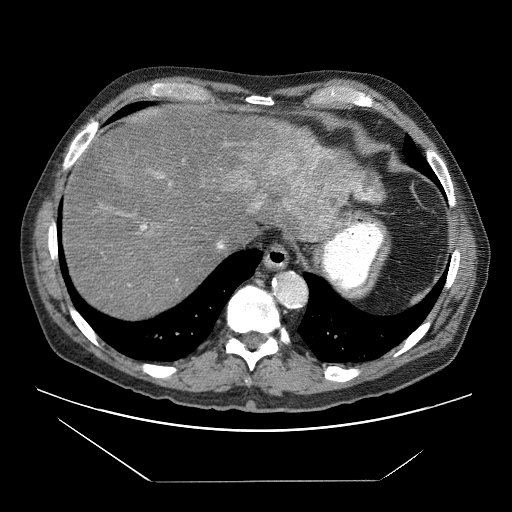
Contrast-enhanced abdominal CT (liver protocol), one axial slice; slice 60 of 83 in the series (ordered by position); soft-tissue window (W 400 / L 40 HU); 512 × 512 image matrix. From the clinical record (not read from this slice): diagnosis: hepatocellular carcinoma (patient treated with transarterial chemoembolisation; whether this scan precedes or follows treatment is not stated here); TNM stage (as recorded): Stage-IVB; Child-Pugh class: B; tumour differentiation: poorly differentiated.
Outlined on this slice (semi-automatic segmentation, software-assisted and operator-edited):
- liver parenchyma outside the tumour (the mass and vessels are separate outlines, so this box may not span the whole liver): box from (x=62, y=118) to (x=382, y=318) px
- mass: (x=232, y=130)–(x=382, y=239)
- liver vessels: (x=123, y=172)–(x=373, y=249)